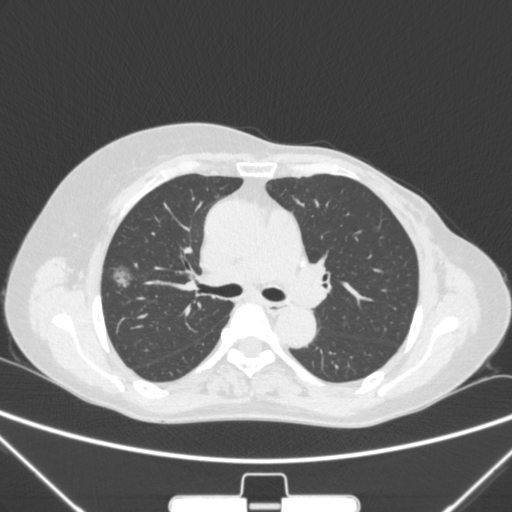
Chest CT, one axial slice; slice 159 of 265 in the series (ordered by position); 120 kVp; lung window (W 1500 / L -600 HU); 1 mm slice thickness; 512 × 512 image matrix. Female patient, age 64 years. Case-level facts recorded for this patient, not image findings: clinical TNM (as recorded): T1c N0 M0; histopathological grade: G1-2.
Outlined on this slice (bounding box drawn by a radiologist):
- lung tumour (recorded histology: adenocarcinoma): bounding box (x1, y1, x2, y2) in pixels: (105, 260, 150, 303)